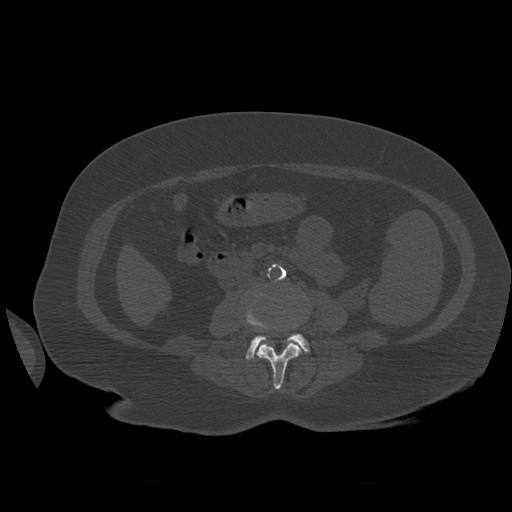
CT including the spine, one axial slice. Slice 219 of 399 in the series (ordered by position). Reconstruction kernel STANDARD. Bone window (W 1800 / L 400 HU). 1.25 mm slice thickness. 512 × 512 image matrix. Patient age 81 years. From the clinical record (not read from this slice): primary cancer: renal.
Structures marked on this image (semi-automatic segmentation, software-assisted and operator-edited):
- L3 vertebra: bounding box [x1, y1, x2, y2] px = [255, 340, 302, 390]
- L4 vertebra: [246, 314, 310, 360]